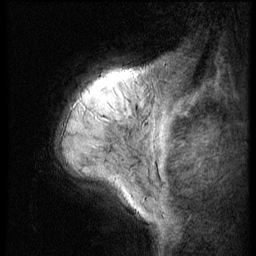
Breast MRI (dynamic contrast-enhanced), one sagittal slice; position 8 of 56 along the scan axis; 3 images stored at this slice position (order not interpretable as contrast timing); 1.5 T; TE 4.2 ms, TR 9 ms; 2.5 mm slice thickness; 256 × 256 image matrix, field of view 180 × 180 mm. Female patient, age 50 years. Case-level facts recorded for this patient, not image findings: setting: breast cancer imaged before/during neoadjuvant chemotherapy; receptor status: triple-negative.
Annotated regions visible in this slice (semi-automatically segmented with operator editing):
- analysis volume of interest (the breast-tissue region the enhancement analysis was run in; not a lesion): box from (x=50, y=53) to (x=135, y=191) px
- tumour enhancement mask (voxels above the 140 % enhancement threshold inside the analysis volume of interest): (x=87, y=104)–(x=100, y=125)